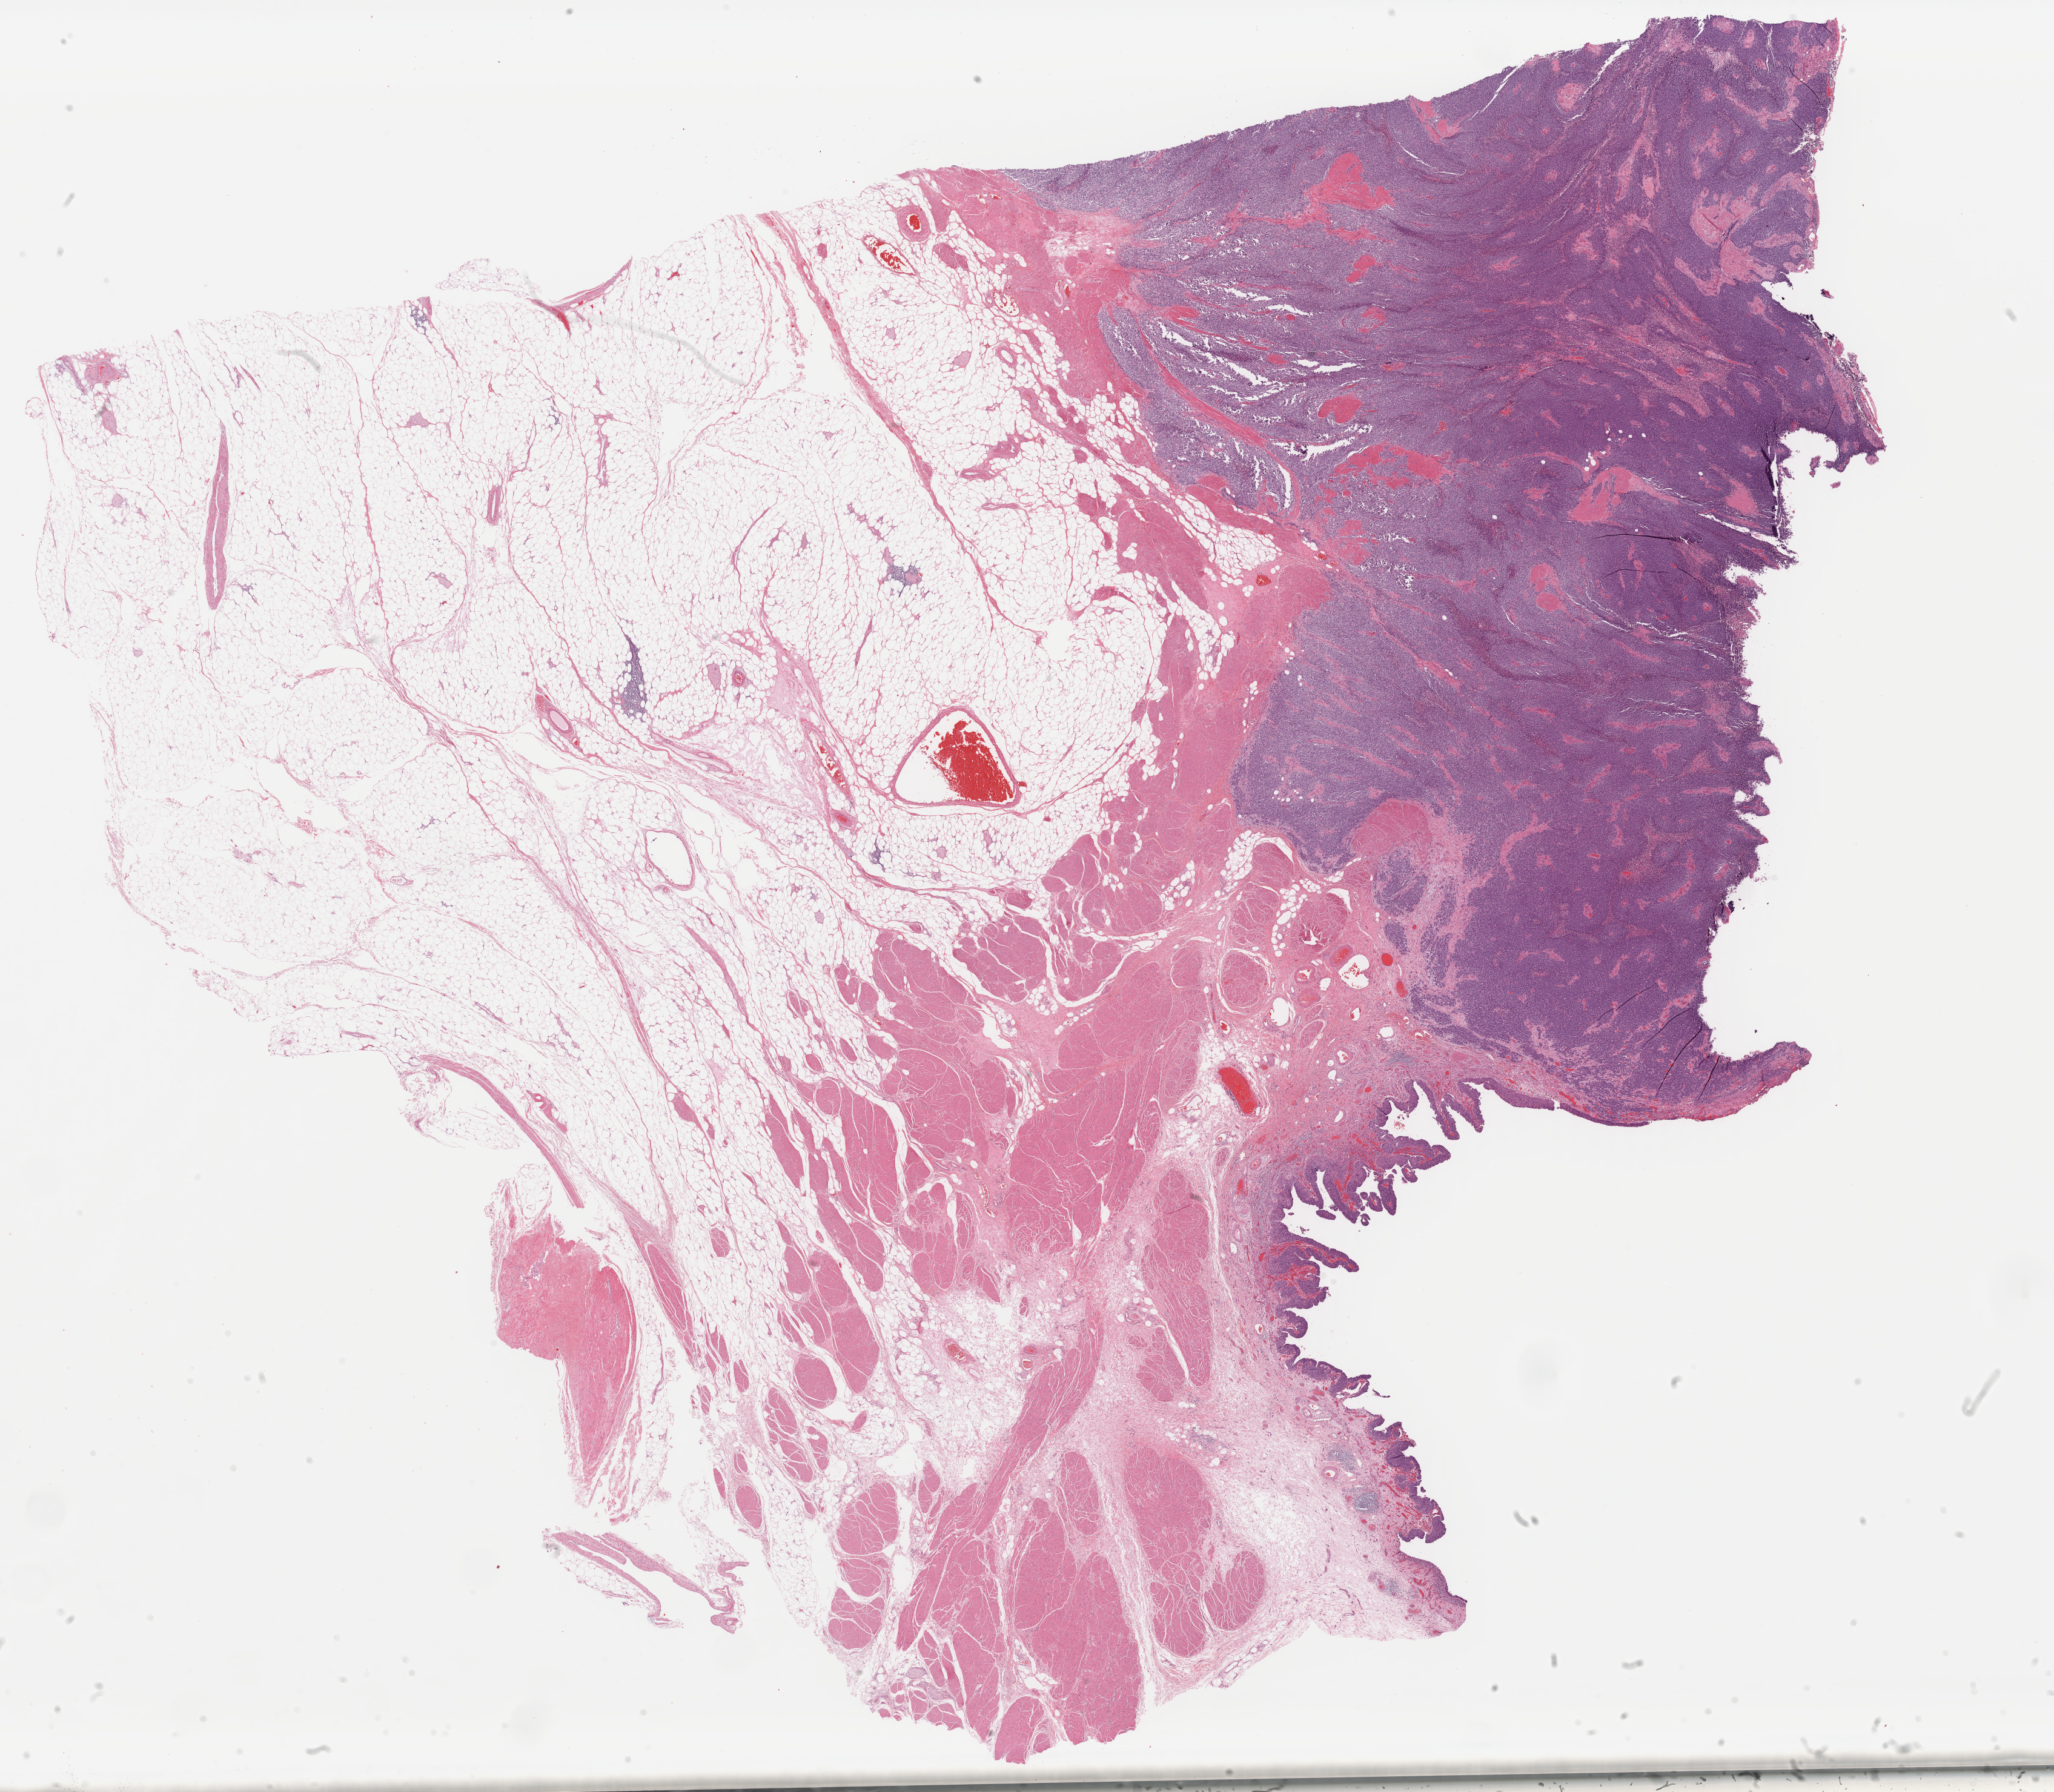
Whole-slide histology image, H&E-stained, a low-resolution overview of the entire scanned area, about 26.8 x 23.3 mm (acquisition: 40x scan), FFPE section, sample: primary tumour, bladder. Patient: male, age at initial diagnosis 54 years. Histologic grade: high grade.
Lymph nodes positive (case pathology): 0 of 12 examined. Pathologic diagnosis: Transitional cell carcinoma. AJCC pathologic stage: III (7th edition).